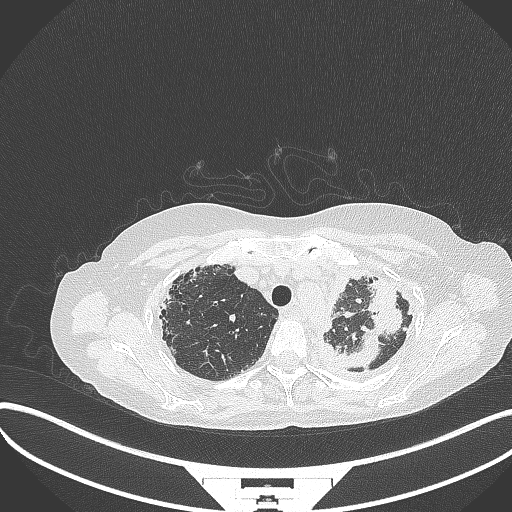
Chest CT, one axial slice. Position 276 of 373 along the scan axis. 120 kVp. Lung window (W 1500 / L -600 HU). 1 mm slice thickness. 512 × 512 image matrix. Female patient, age 56 years. From the clinical record (not read from this slice): clinical TNM (as recorded): T1 N0 M0.
Structures marked on this image (bounding box drawn by a radiologist):
- lung tumour (recorded histology: adenocarcinoma): bounding box [x1, y1, x2, y2] px = [338, 271, 408, 369]